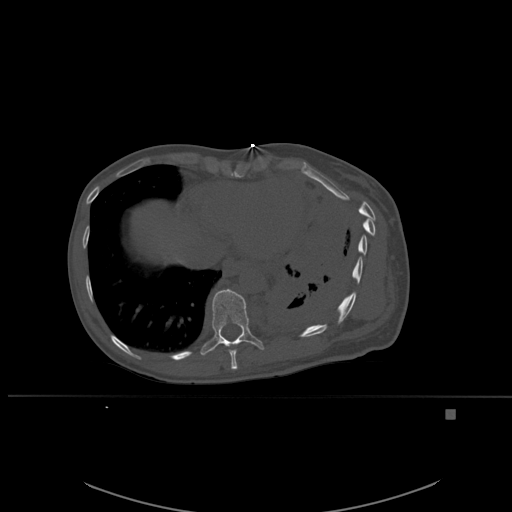
CT including the spine, one axial slice. Slice 321 of 537 in the series (ordered by position). Bone window (W 1800 / L 400 HU). 1.5 mm slice thickness. 512 × 512 image matrix, field of view 440 × 440 mm. Patient: female, 45 years. From the clinical record (not read from this slice): primary cancer: lung.
Structures marked on this image (semi-automatically segmented with operator editing):
- T10 vertebra: bounding box (x1, y1, x2, y2) in pixels: (200, 288, 264, 356)
- T9 vertebra: (229, 345, 238, 370)